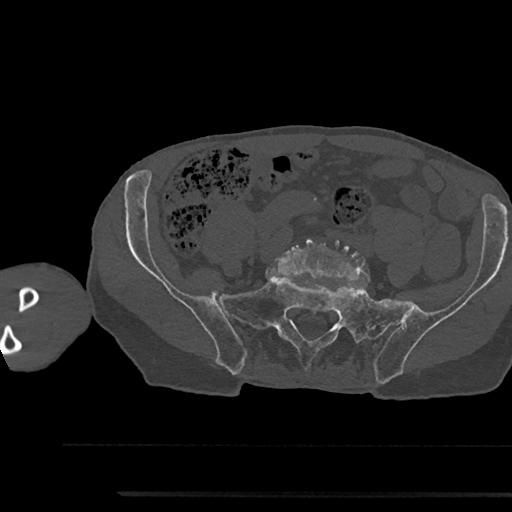
CT including the spine, one axial slice; slice 305 of 797 in the series (ordered by position); reconstruction kernel Br40s/3; bone window (W 1800 / L 400 HU); 512 × 512 image matrix. Male patient, age 79 years. From the clinical record (not read from this slice): primary cancer: prostate.
Structures marked on this image (semi-automatic segmentation, software-assisted and operator-edited):
- L5 vertebra: bounding box <276,235,370,281> (left, top, right, bottom; pixels)